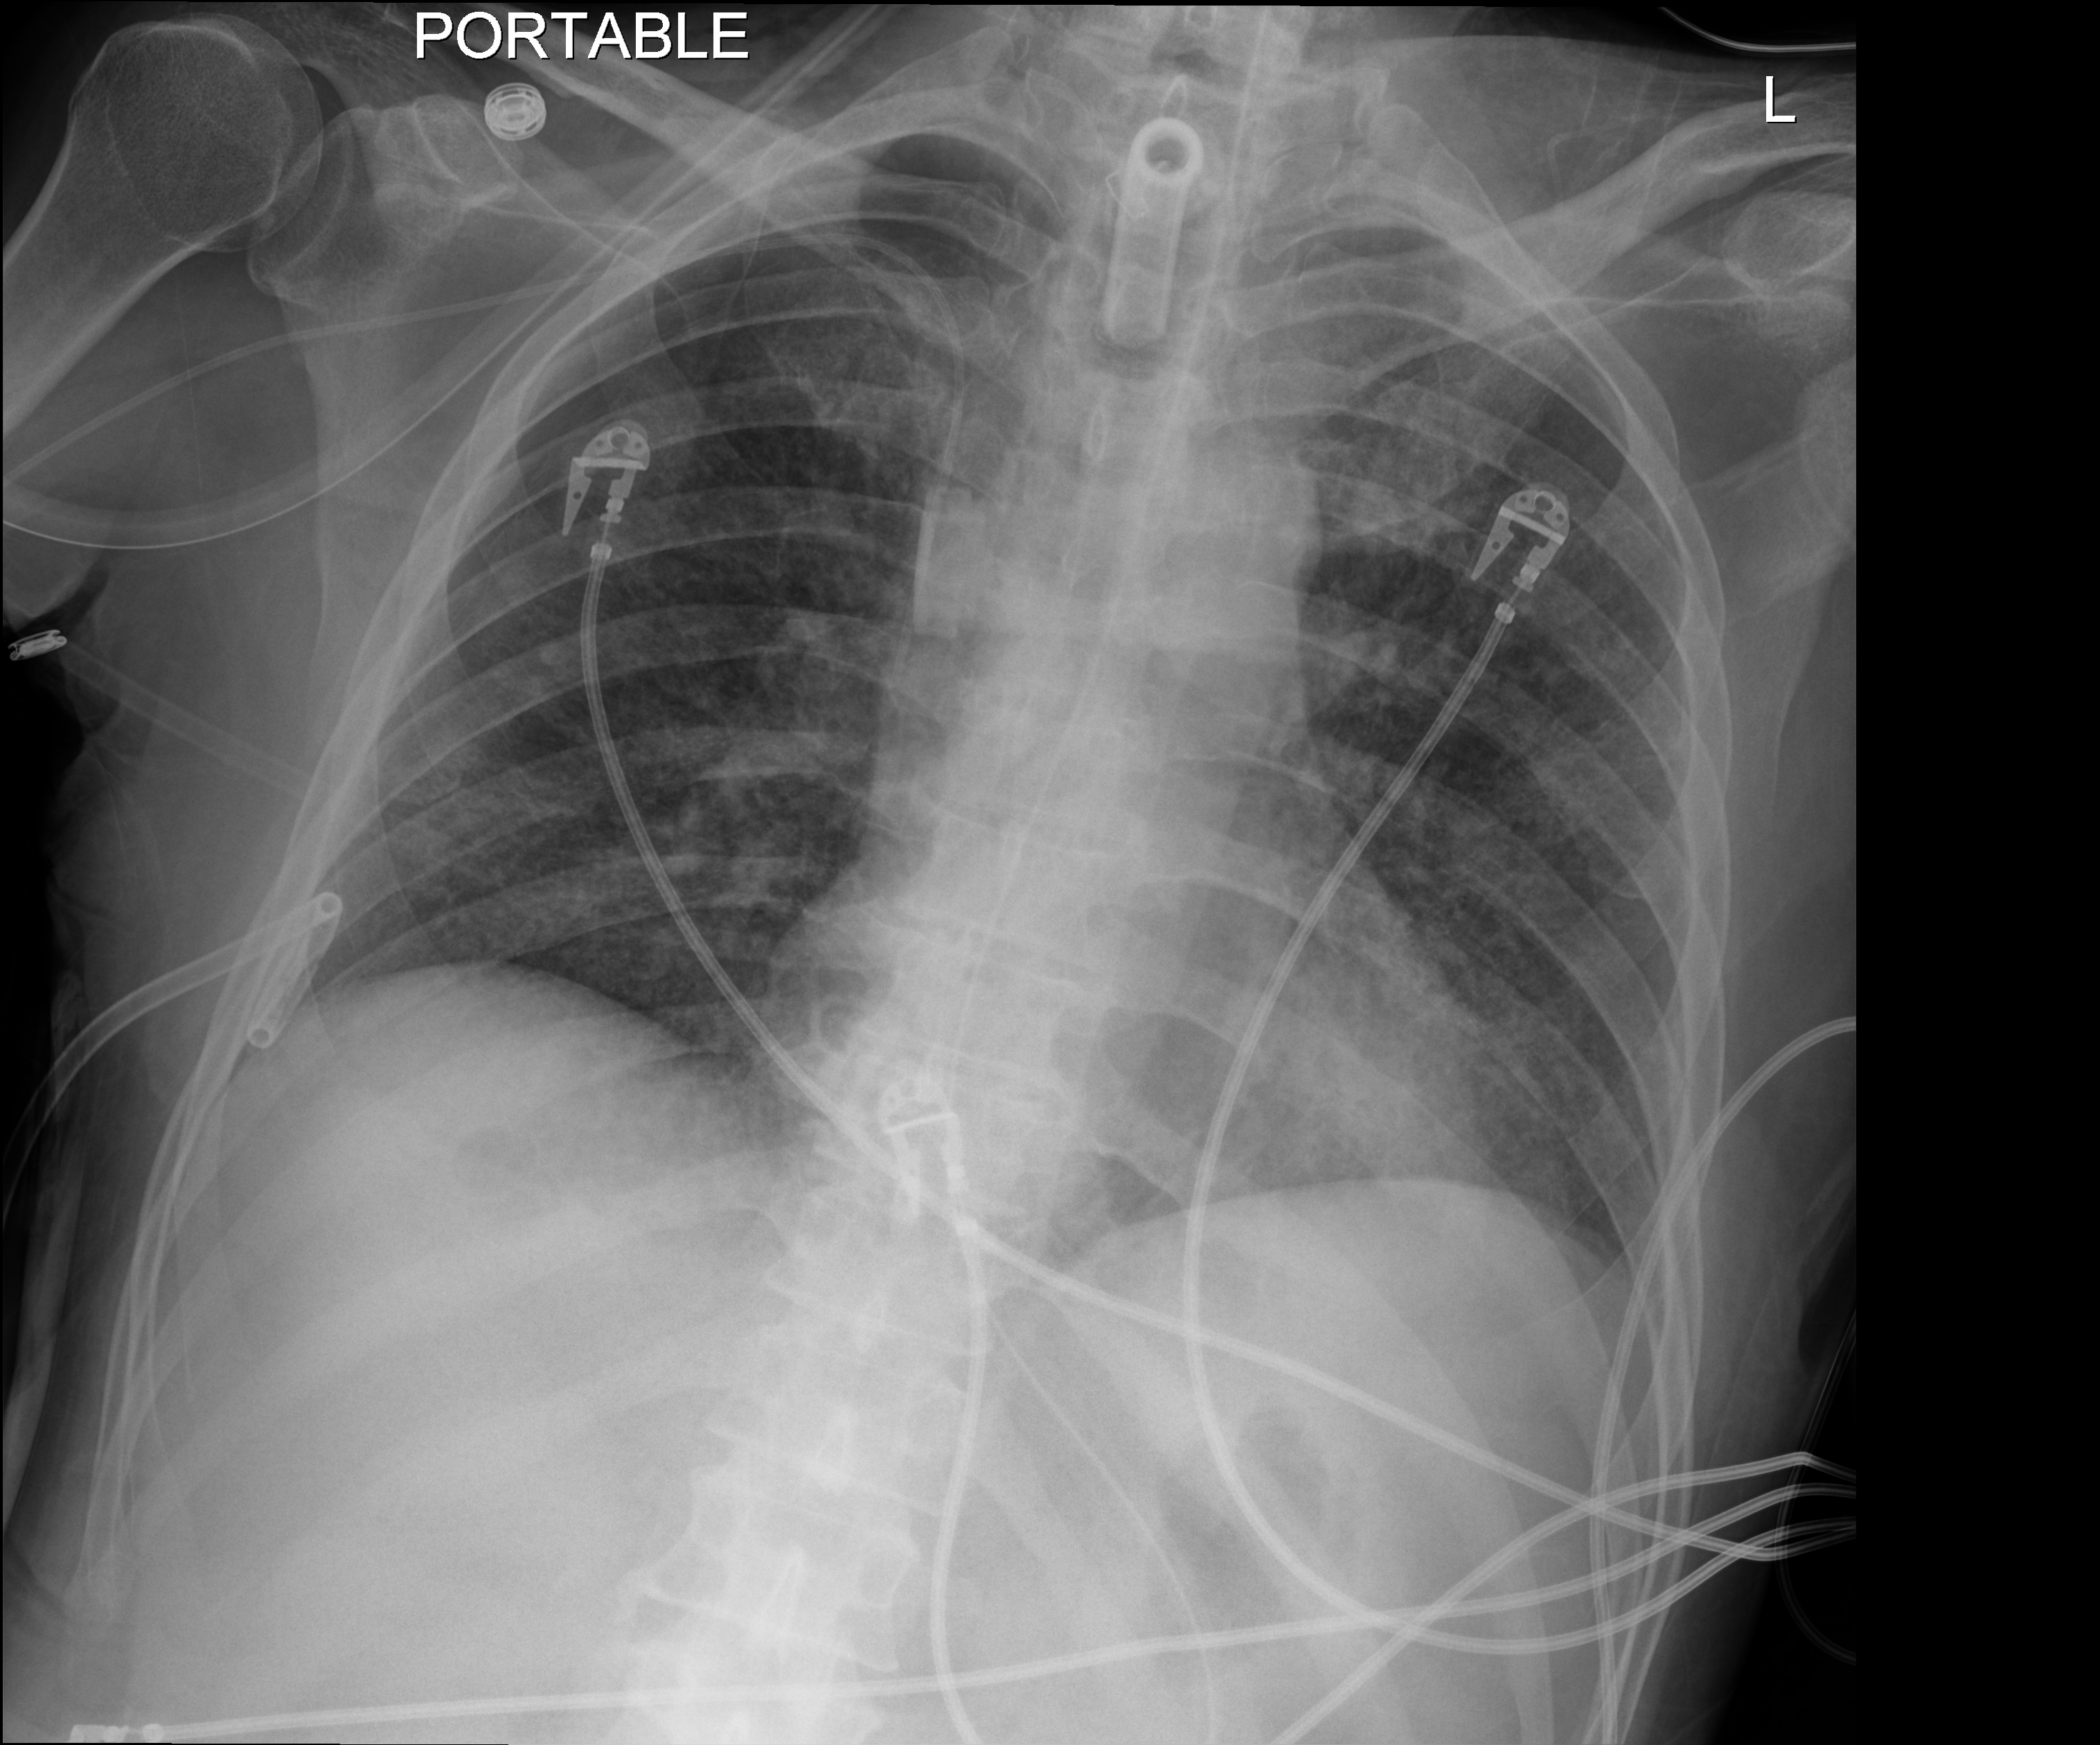
Chest X-ray (portable). Patient hospitalised with COVID-19; male, aged 18–59 years.
Hospital-stay facts (about this admission, not read from this image; timing relative to this image not recorded):
- diabetes (admission record): no